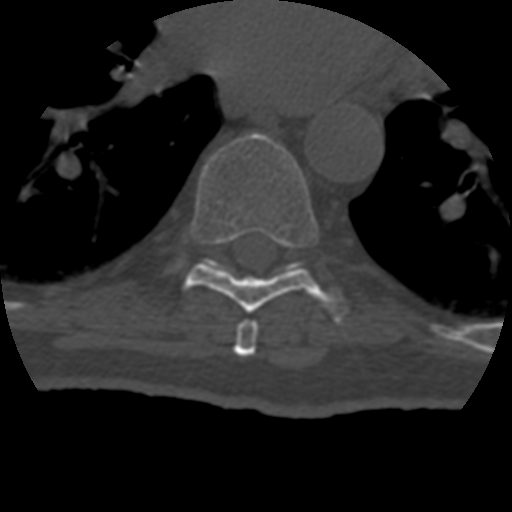
CT including the spine, one axial slice; bone window (W 1800 / L 400 HU); 512 × 512 image matrix. Patient age 69 years. Case-level facts recorded for this patient, not image findings: primary cancer: prostate.
Structures marked on this image (semi-automatic segmentation, software-assisted and operator-edited):
- T7 vertebra: bounding box [x1, y1, x2, y2] px = [234, 320, 259, 357]
- T8 vertebra: [185, 133, 348, 321]
- T9 vertebra: [209, 257, 213, 259]